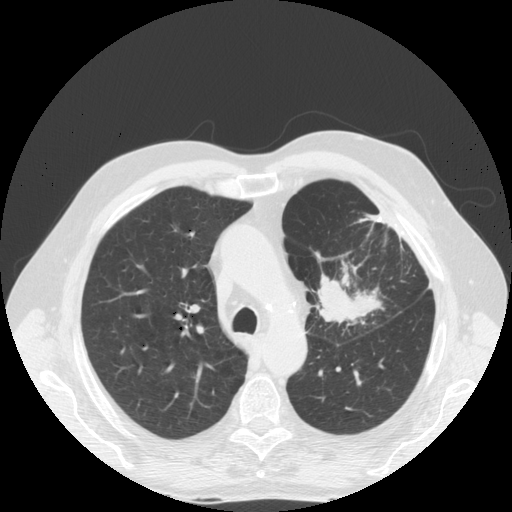
Axial slice from a low-dose chest CT screening exam; baseline screening round; lung window (W 1500 / L -600 HU); 512 × 512 image matrix, field of view 380 × 380 mm. Male participant, aged 70 years at enrolment. Former smoker at enrolment.
• Expert reader's lesion annotation, bounding box <295,256,393,344> (left, top, right, bottom; pixels).
• Screening reader's record for this exam (one nodule recorded; not confirmed to be the boxed lesion): non-calcified nodule or mass ≥4 mm, left upper lobe, 46 × 31 mm, spiculated (stellate) margins, soft tissue attenuation.
• Participant outcome: lung cancer diagnosed 78 days after this screen — squamous cell carcinoma, NOS, left upper lobe, poorly differentiated (G3), stage IIIB (AJCC 6th edition), 46 mm at pathology.